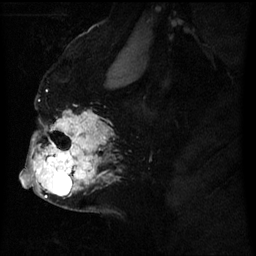
Breast MRI (dynamic contrast-enhanced), one sagittal slice; position 39 of 60 along the scan axis; dynamic contrast-enhanced series, image 2 of 3 at this slice position (ordered by acquisition); 1.5 T; TE 4.2 ms, TR 8 ms; 2.5 mm slice thickness; 256 × 256 image matrix, field of view 200 × 200 mm. Patient: female, 50 years.
Outlined on this slice (semi-automatic segmentation, software-assisted and operator-edited):
- analysis volume of interest (the breast-tissue region the enhancement analysis was run in; not a lesion): box from (x=24, y=116) to (x=107, y=199) px
- tumour enhancement mask (voxels above the 70 % enhancement threshold inside the analysis volume of interest): (x=24, y=124)–(x=102, y=187)